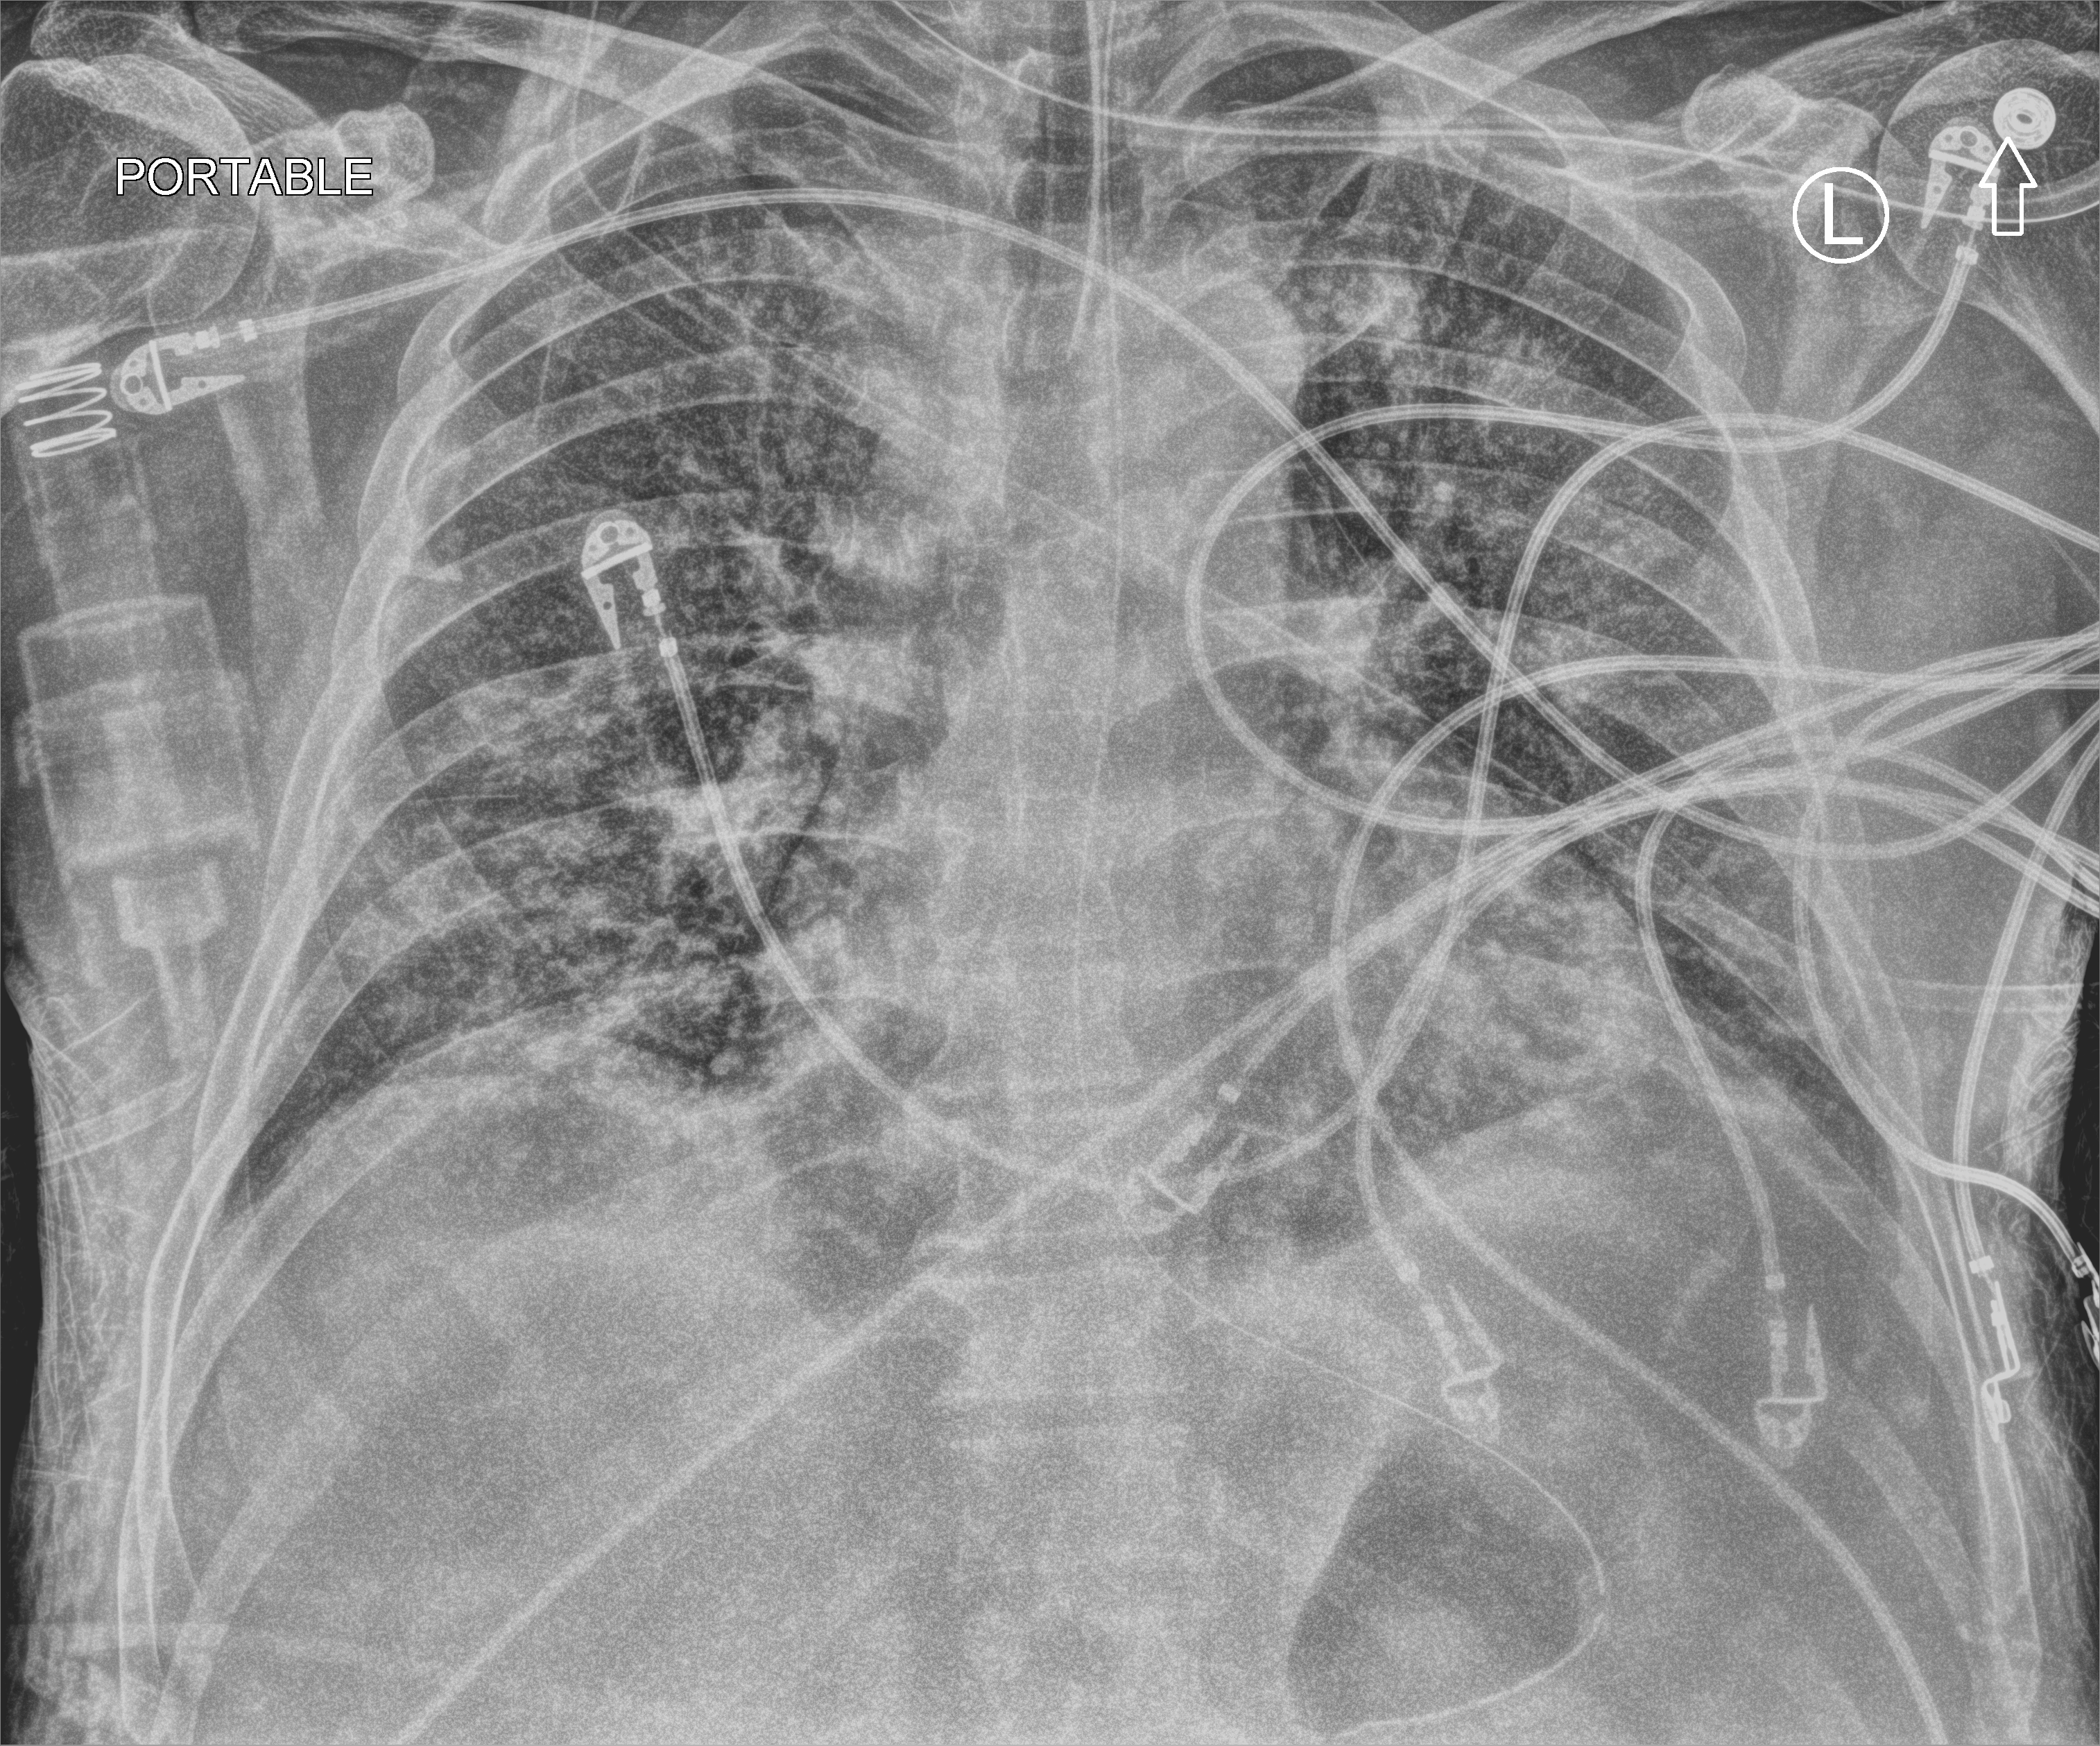
Chest X-ray (portable), anteroposterior (AP) projection. Male patient hospitalised with COVID-19, age 18–59 years.
From the hospital-stay record, not from the radiograph (when in the stay this image was taken is not recorded):
- COPD (admission record): no